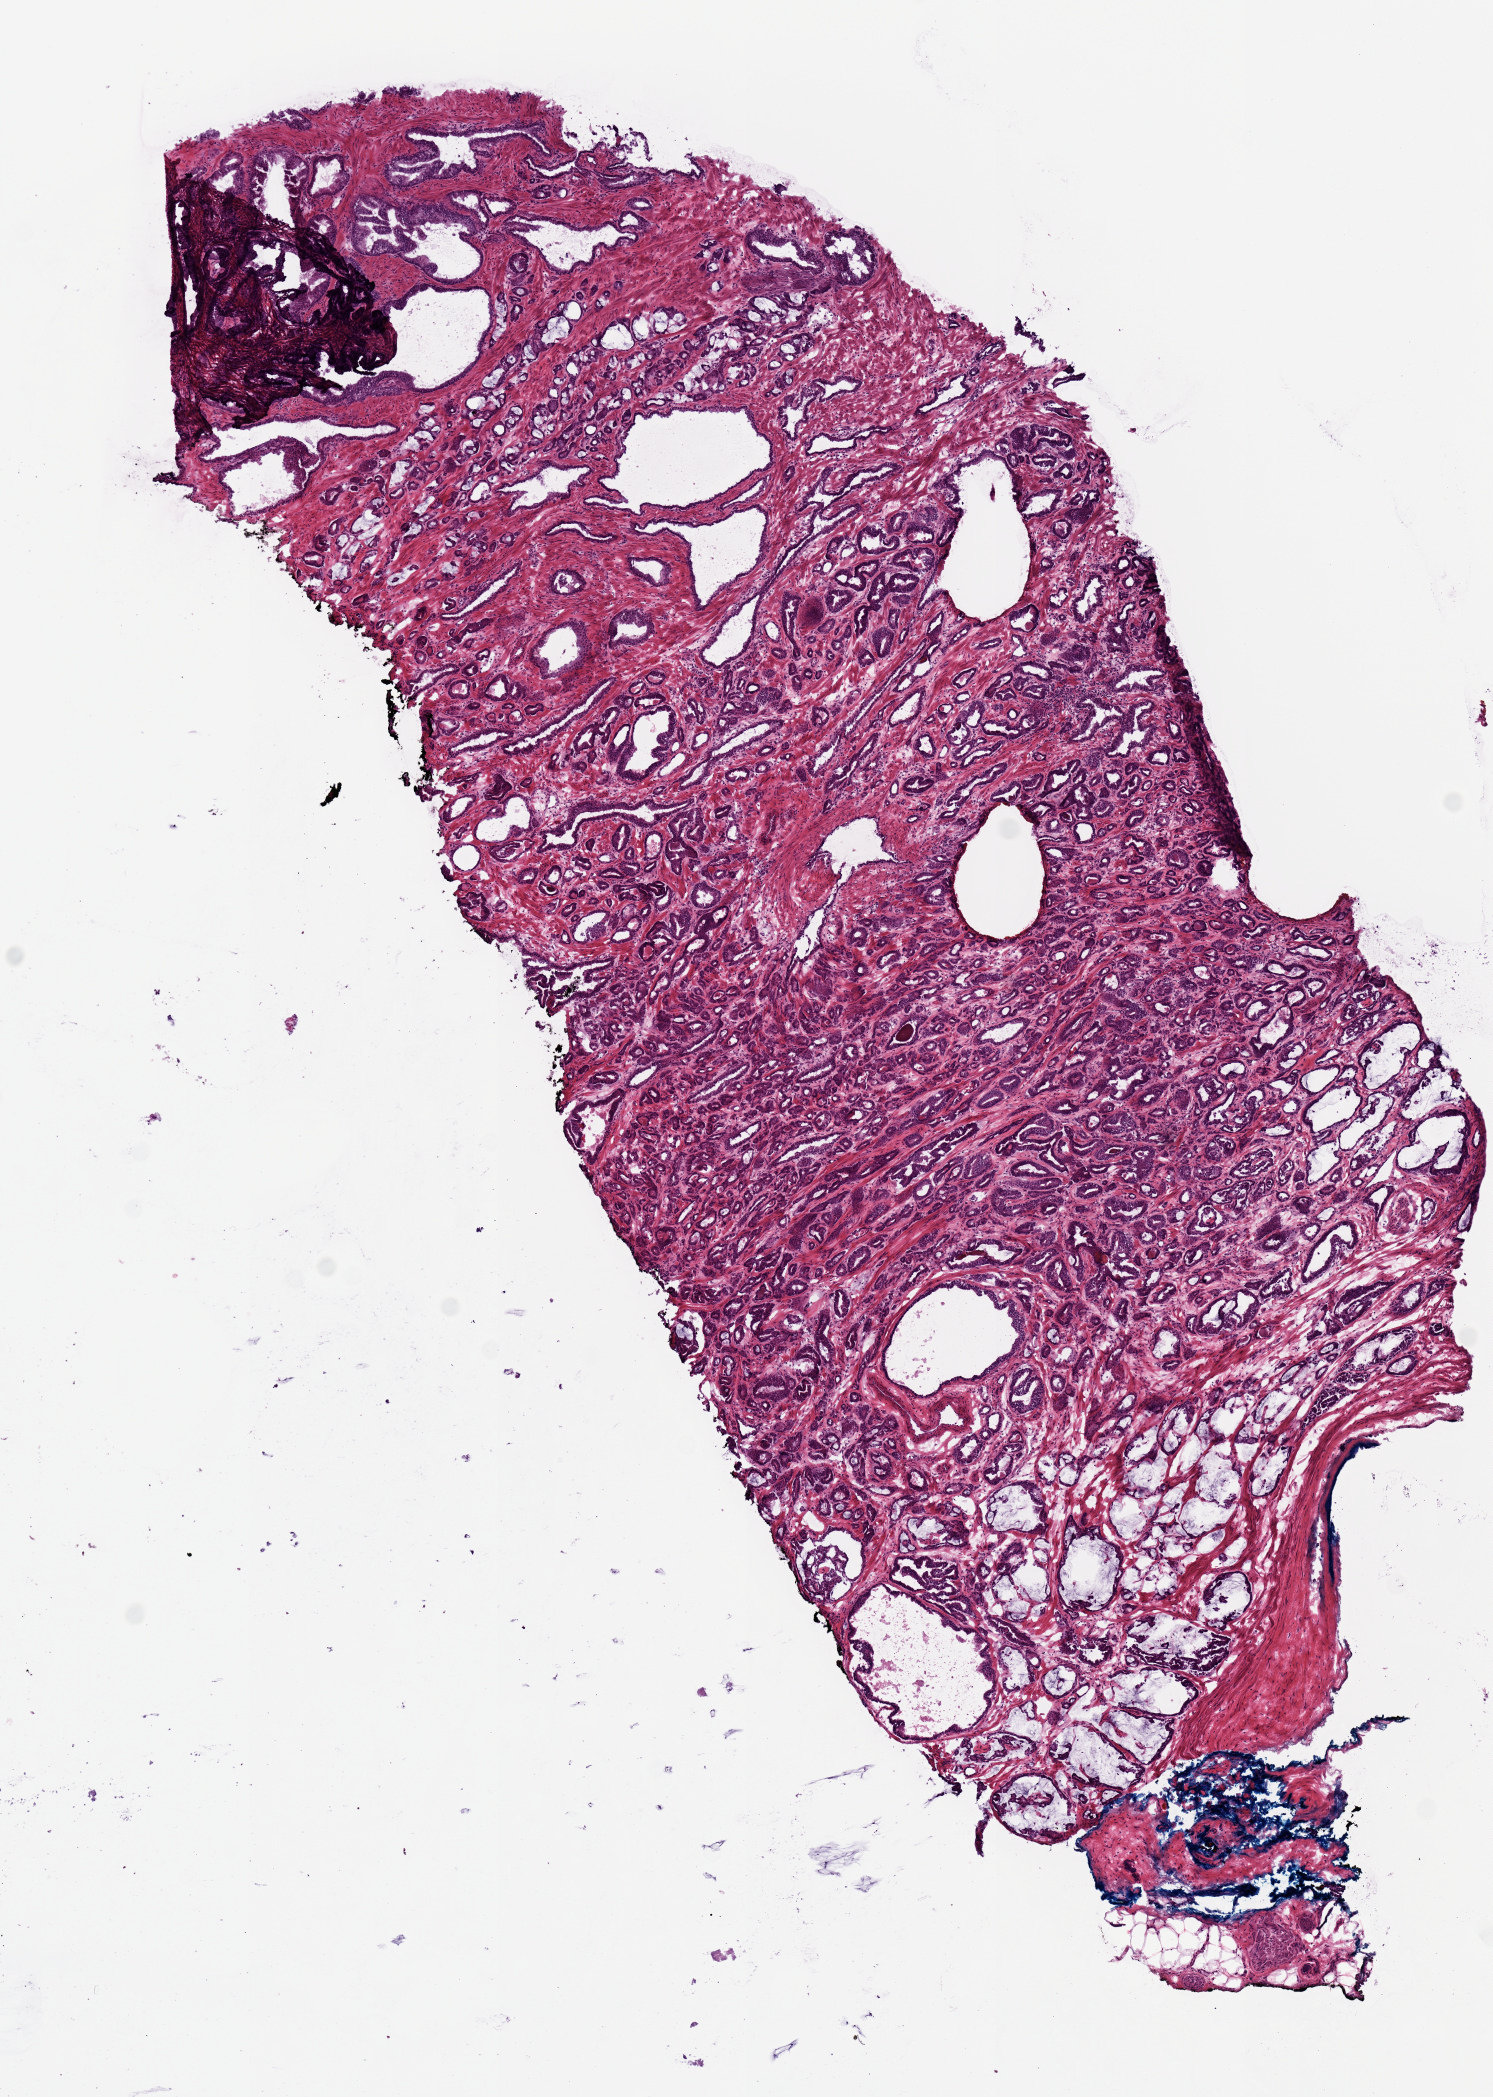
H&E-stained whole-slide image — whole scanned area (about 5.9 x 8.3 mm, slide scanned at 20x) shown as a low-resolution overview, frozen section from the top of the tissue portion, primary tumour sample from the prostate. Male patient; age at initial diagnosis 53 years. Gleason score: 8 (4+4). Pathologist review of this section (percent, as recorded): tumour cells 85%, tumour nuclei 85%, normal cells 5%, stromal cells 10%, necrosis 0%.
* lymph nodes positive (case pathology): 0 of 3 examined
* histologic diagnosis: Acinar cell carcinoma (prostate gland)